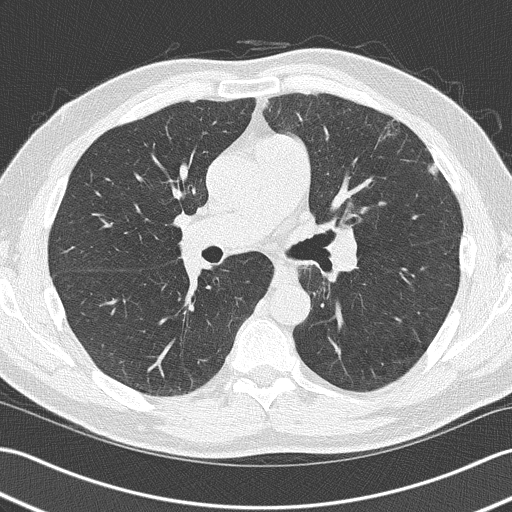
Axial slice from a low-dose chest CT screening exam, baseline screening round, lung window (W 1500 / L -600 HU), lung (sharp) reconstruction kernel (B50f). Male participant, aged 58 years at enrolment. Current smoker at enrolment.
Expert-annotated lung lesion, bounding box (x1, y1, x2, y2) in pixels: (410, 150, 461, 193). Reader record for this screening exam (exam-level; its link to the box is not recorded): non-calcified nodule or mass ≥4 mm, lingula, 10 × 6 mm, mixed attenuation. Later outcome: lung cancer diagnosed 258 days after this screen — squamous cell carcinoma, NOS, lingula, poorly differentiated (G3), stage IIIB (AJCC 6th edition).